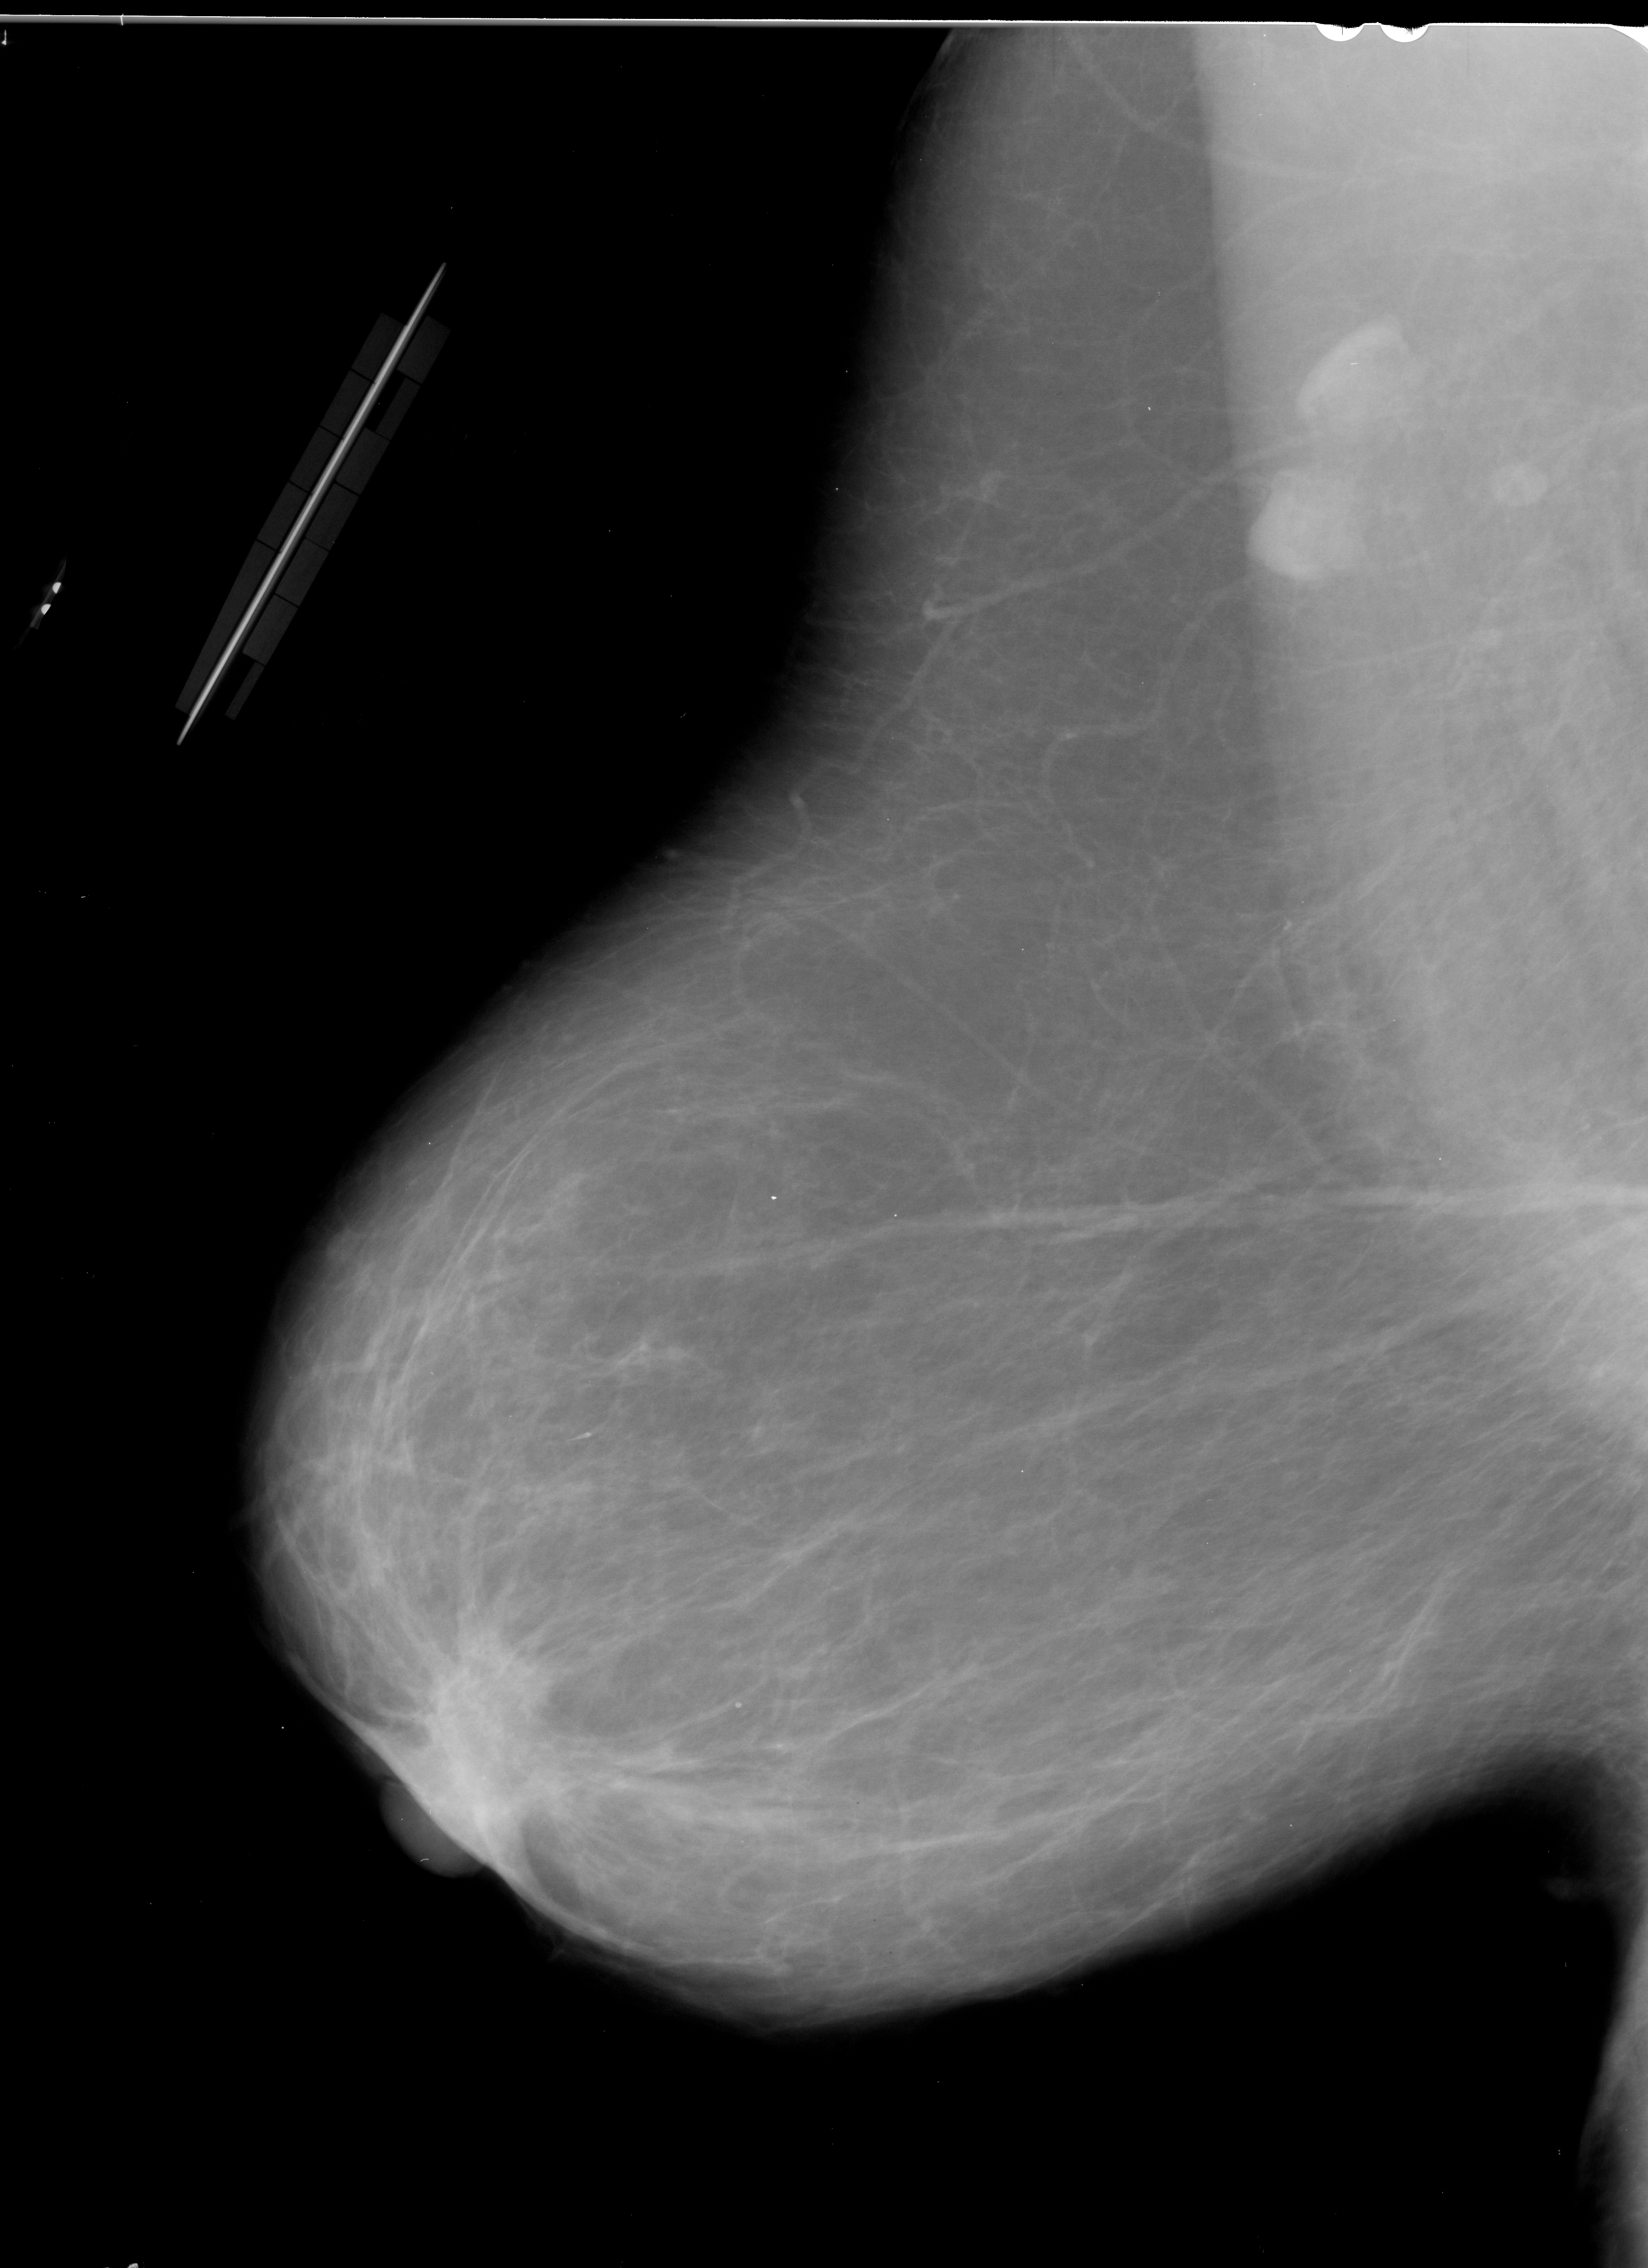
Mammogram (digitized film). Left breast. MLO view. BI-RADS breast density category 2 (scale 1–4). 1648 × 2268 image matrix.
Marked abnormalities (boxes around the expert regions of interest):
- mass, shape irregular, margins spiculated; BI-RADS assessment category 5; pathology (as recorded): malignant: bounding box <436,1623,606,1791> (left, top, right, bottom; pixels)